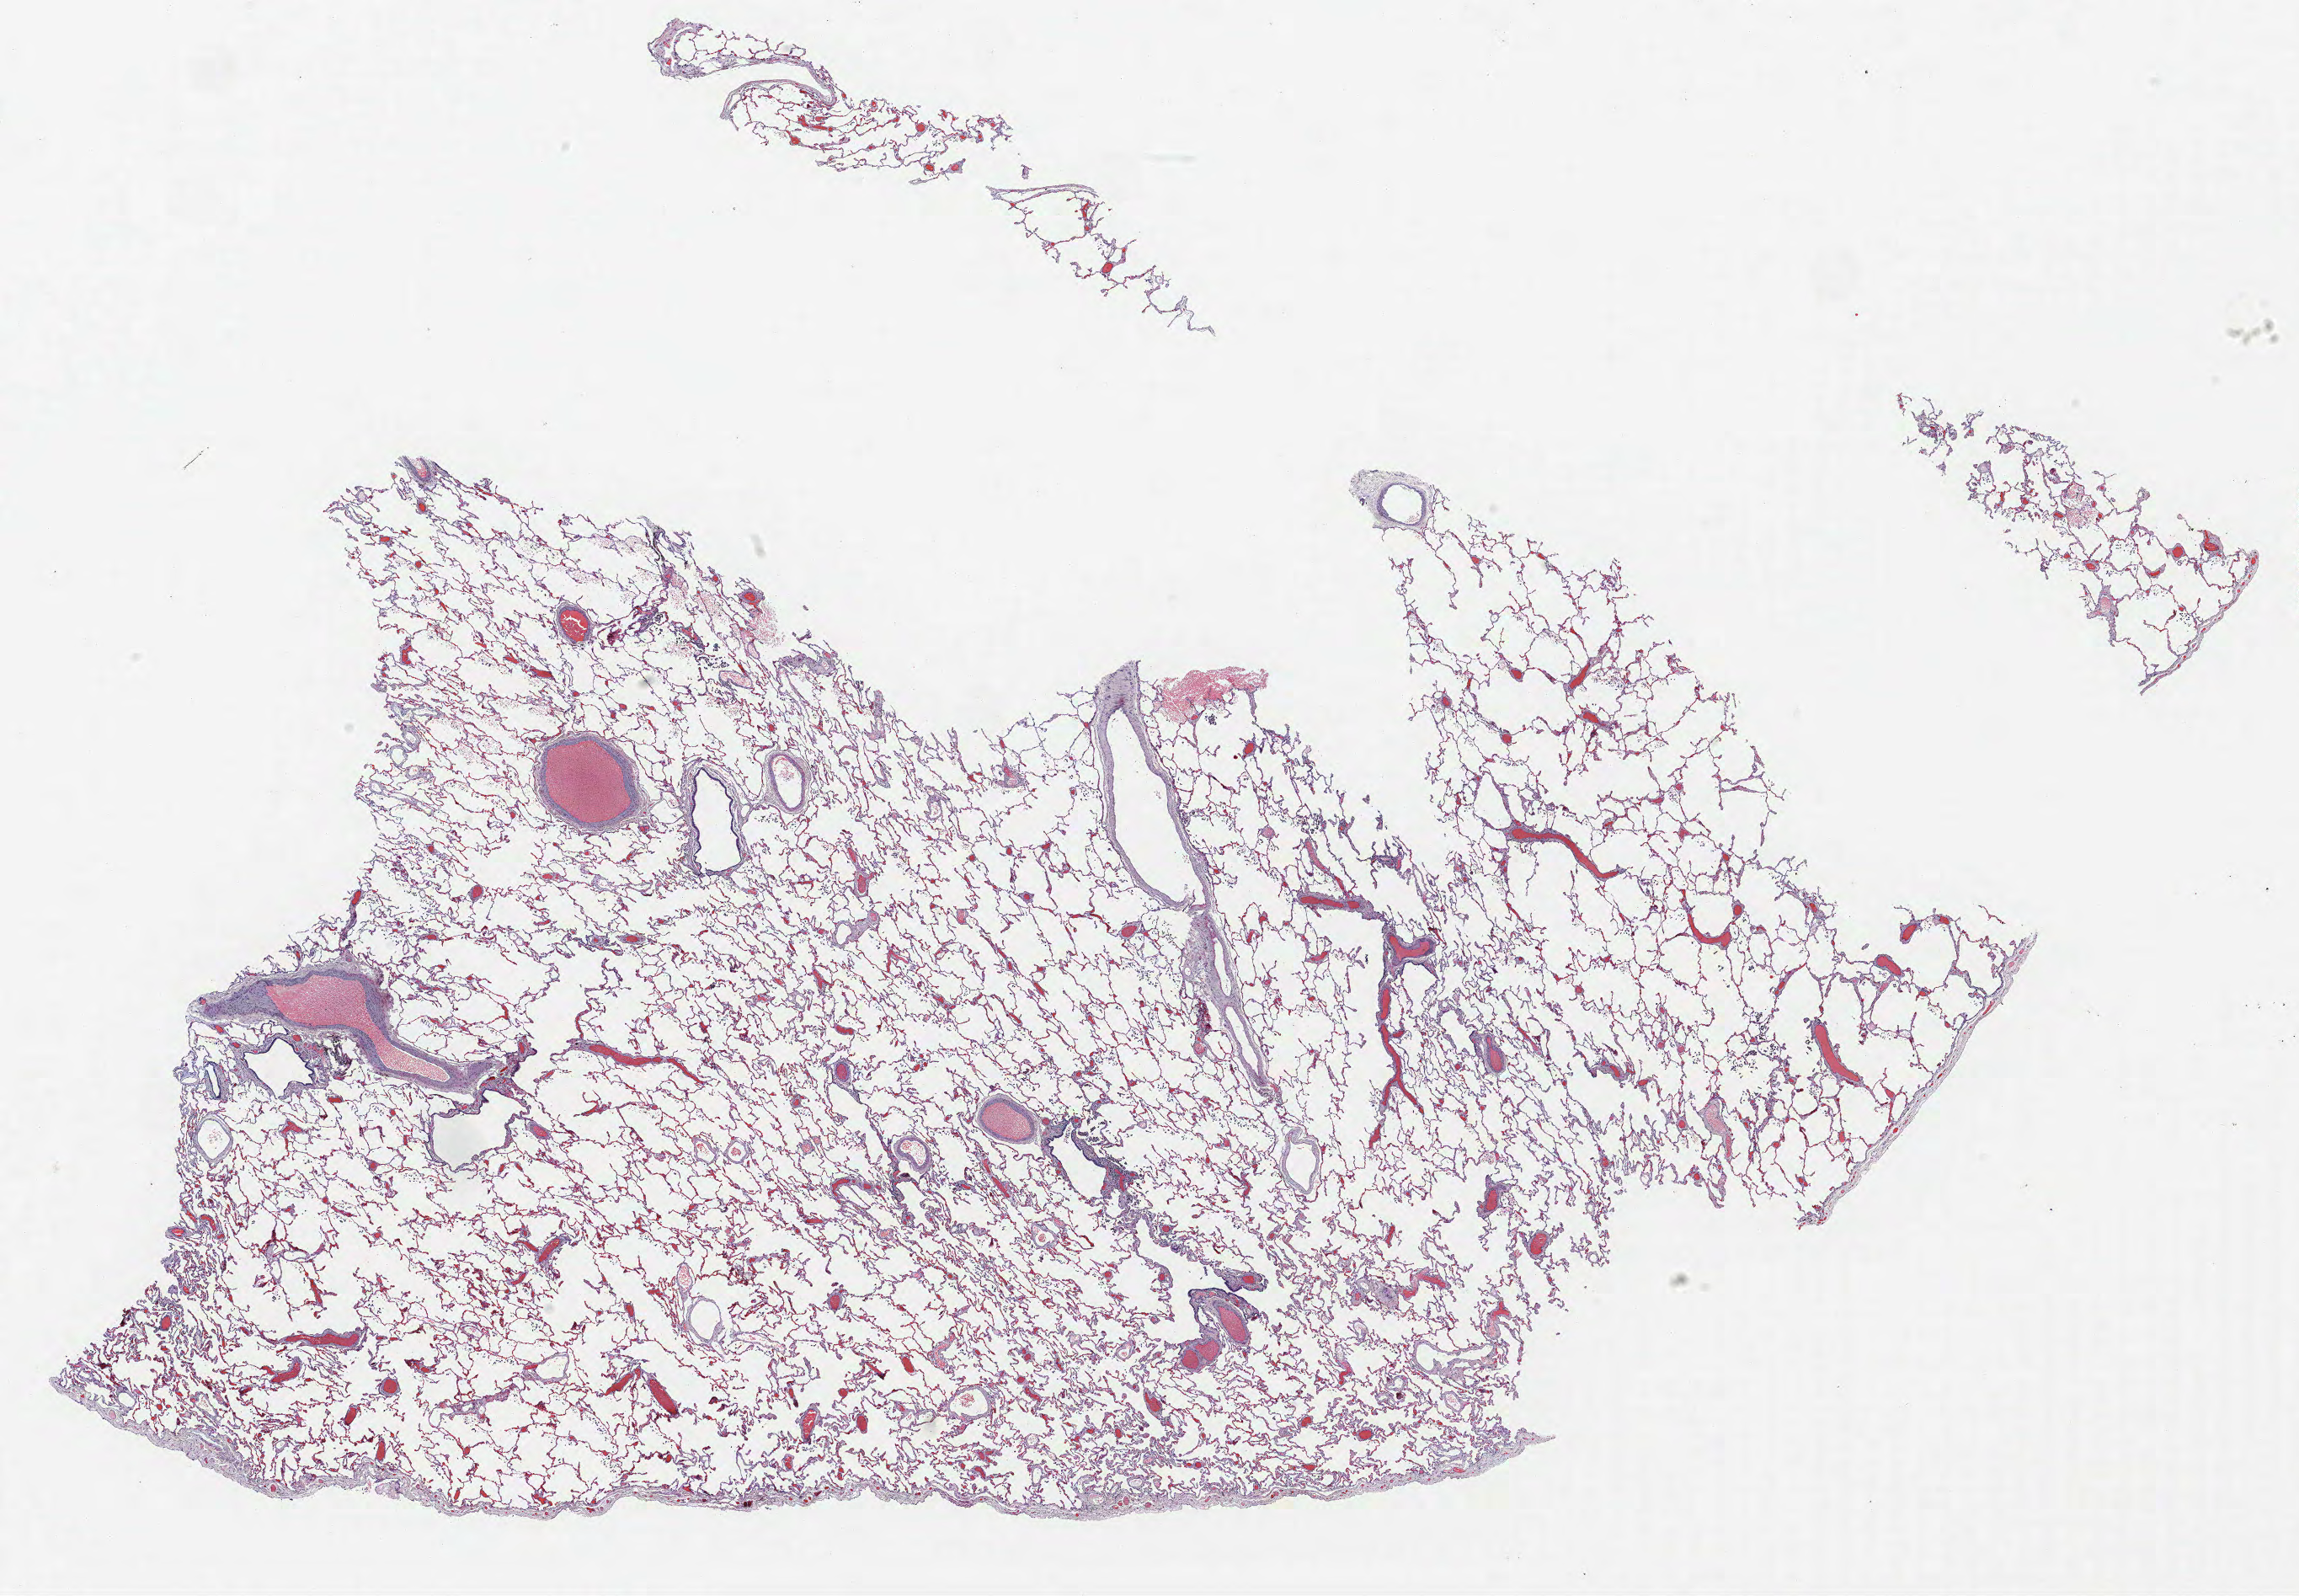
Hematoxylin and eosin (H&E) stained whole-slide image — shown as a low-resolution overview of the whole scanned area (about 21.8 x 15.2 mm). FFPE section. Lung. Female, age 56 at enrolment. Current smoker at enrolment. Grade: well differentiated (G1).
Primary tumour location (clinical record): left lower lobe. Stage (AJCC 6th edition): IA. Tumour size (pathology): 20 mm. ICD-O-3 topography: lower lobe of lung (C34.3). Participant's lung-cancer diagnosis: Bronchiolo-alveolar adenocarcinoma, NOS (ICD-O-3 8250/3).